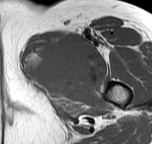
MRI of an extremity soft-tissue mass, one axial slice; position 43 of 57 along the scan axis; MR volume resampled by the dataset authors to the PET/CT grid (not the native acquisition matrix); 152 × 144 image matrix. Female patient. Case-level facts recorded for this patient, not image findings: histological type: pleiomorphic leiomyosarcoma; grade: intermediate; site of the primary tumour: left thigh.
Annotated regions visible in this slice (expert contour drawn on MRI and transferred to this co-registered scan by the dataset authors):
- gross tumour volume including surrounding oedema: bounding box (x1, y1, x2, y2) in pixels: (27, 33, 96, 89)
- gross tumour volume (mass): (27, 33, 96, 89)